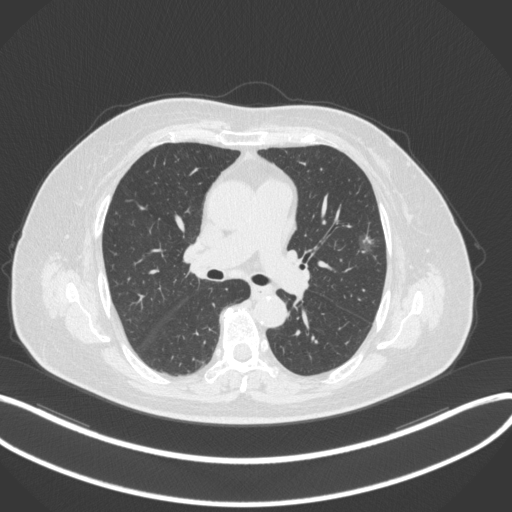
Chest CT, one axial slice. Position 185 of 286 along the scan axis. Reconstruction kernel B31f. 120 kVp. Lung window (W 1500 / L -600 HU). 1 mm slice thickness. 512 × 512 image matrix, field of view 400 × 400 mm. Patient: female, 76 years. From the clinical record (not read from this slice): clinical TNM (as recorded): T1b N0 M0.
Outlined on this slice (bounding box drawn by a radiologist):
- lung tumour (recorded histology: adenocarcinoma): box from (x=350, y=221) to (x=379, y=257) px